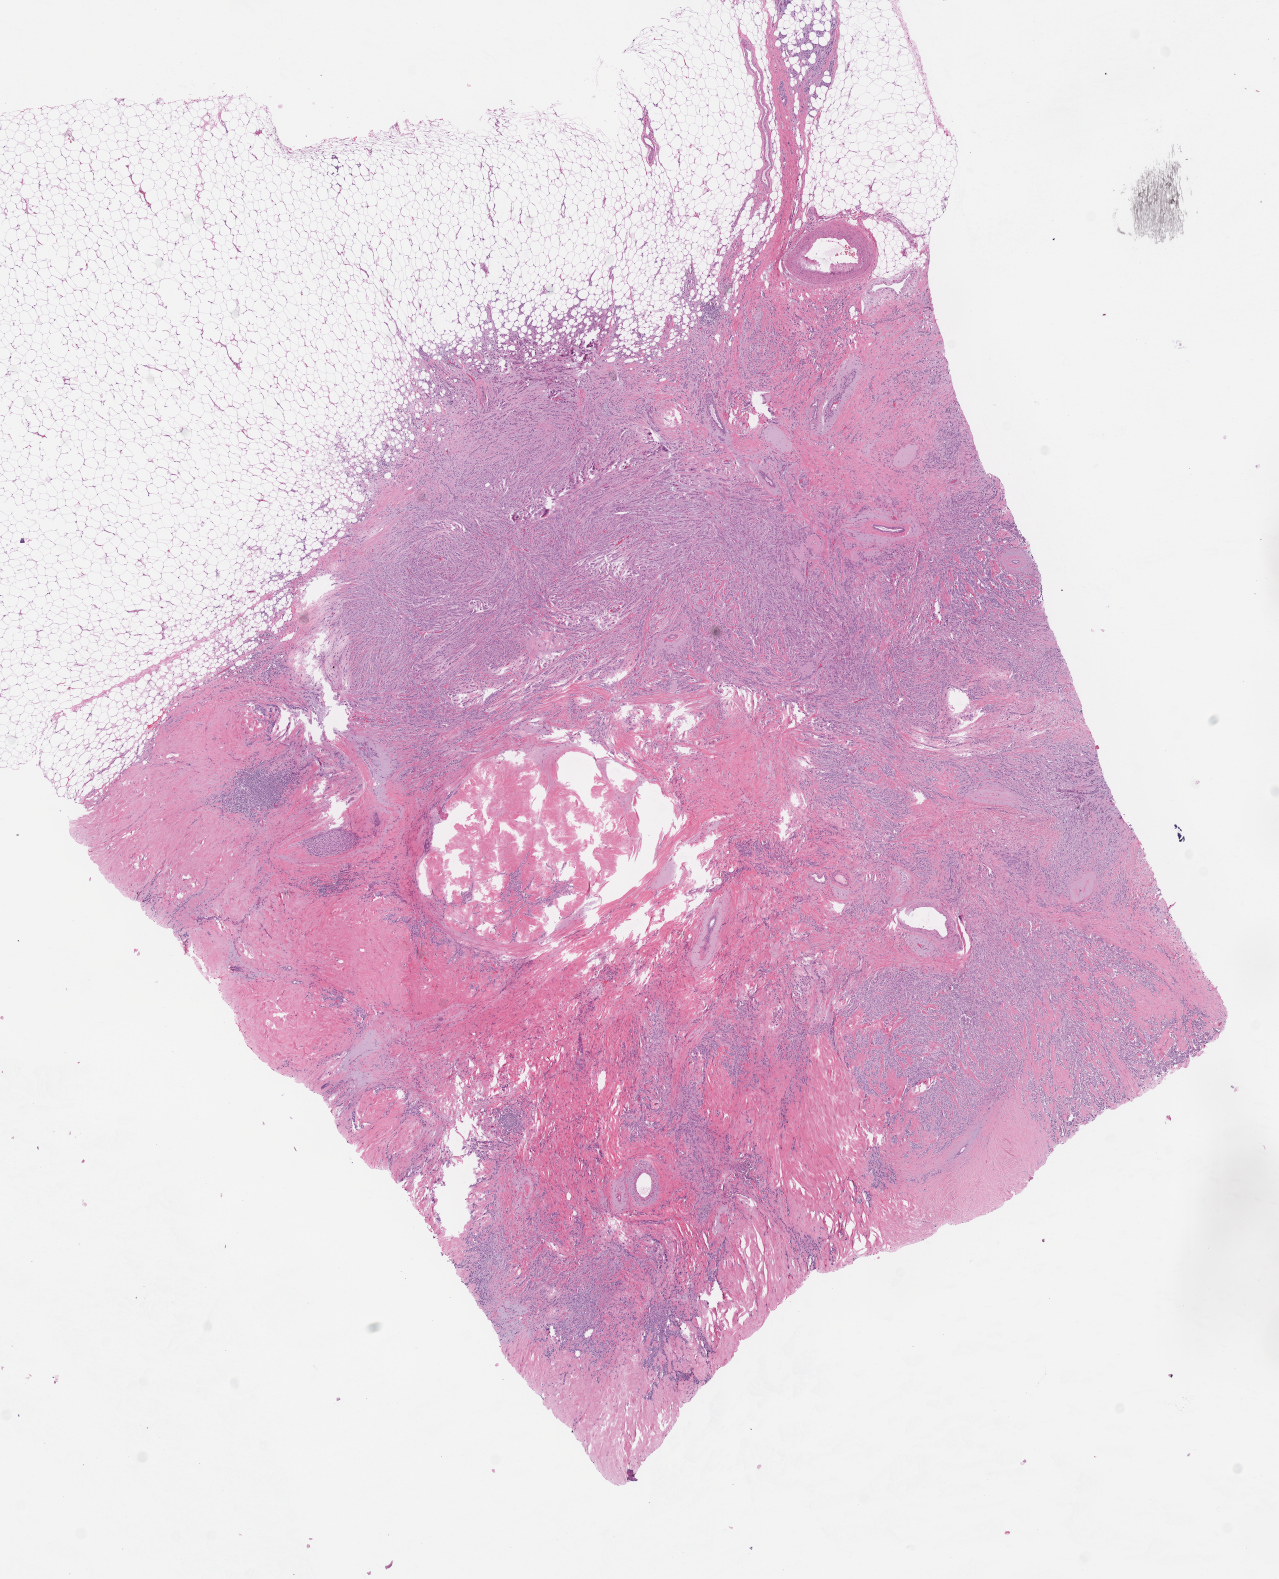
Digitized Hematoxylin and eosin (H&E) stained tissue section (whole slide), whole scanned area (about 10.1 x 12.4 mm, acquisition: 40x scan) shown as a low-resolution overview. Formalin-fixed paraffin-embedded (FFPE) diagnostic section. Sample: primary tumour, breast. Female patient; age at initial diagnosis 76 years.
Diagnosis: Lobular carcinoma, NOS.